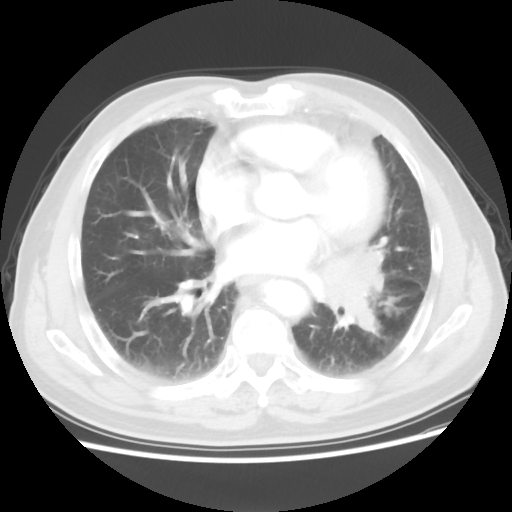
Chest CT, one axial slice; reconstruction kernel STANDARD; 120 kVp; lung window (W 1500 / L -600 HU); 512 × 512 image matrix. Patient: male, 75 years. Case-level facts recorded for this patient, not image findings: clinical TNM (as recorded): T3 N0 M0.
Outlined on this slice (rectangle marked by the reading radiologist):
- lung tumour (recorded histology: squamous cell carcinoma): bounding box (x1, y1, x2, y2) in pixels: (313, 238, 395, 327)